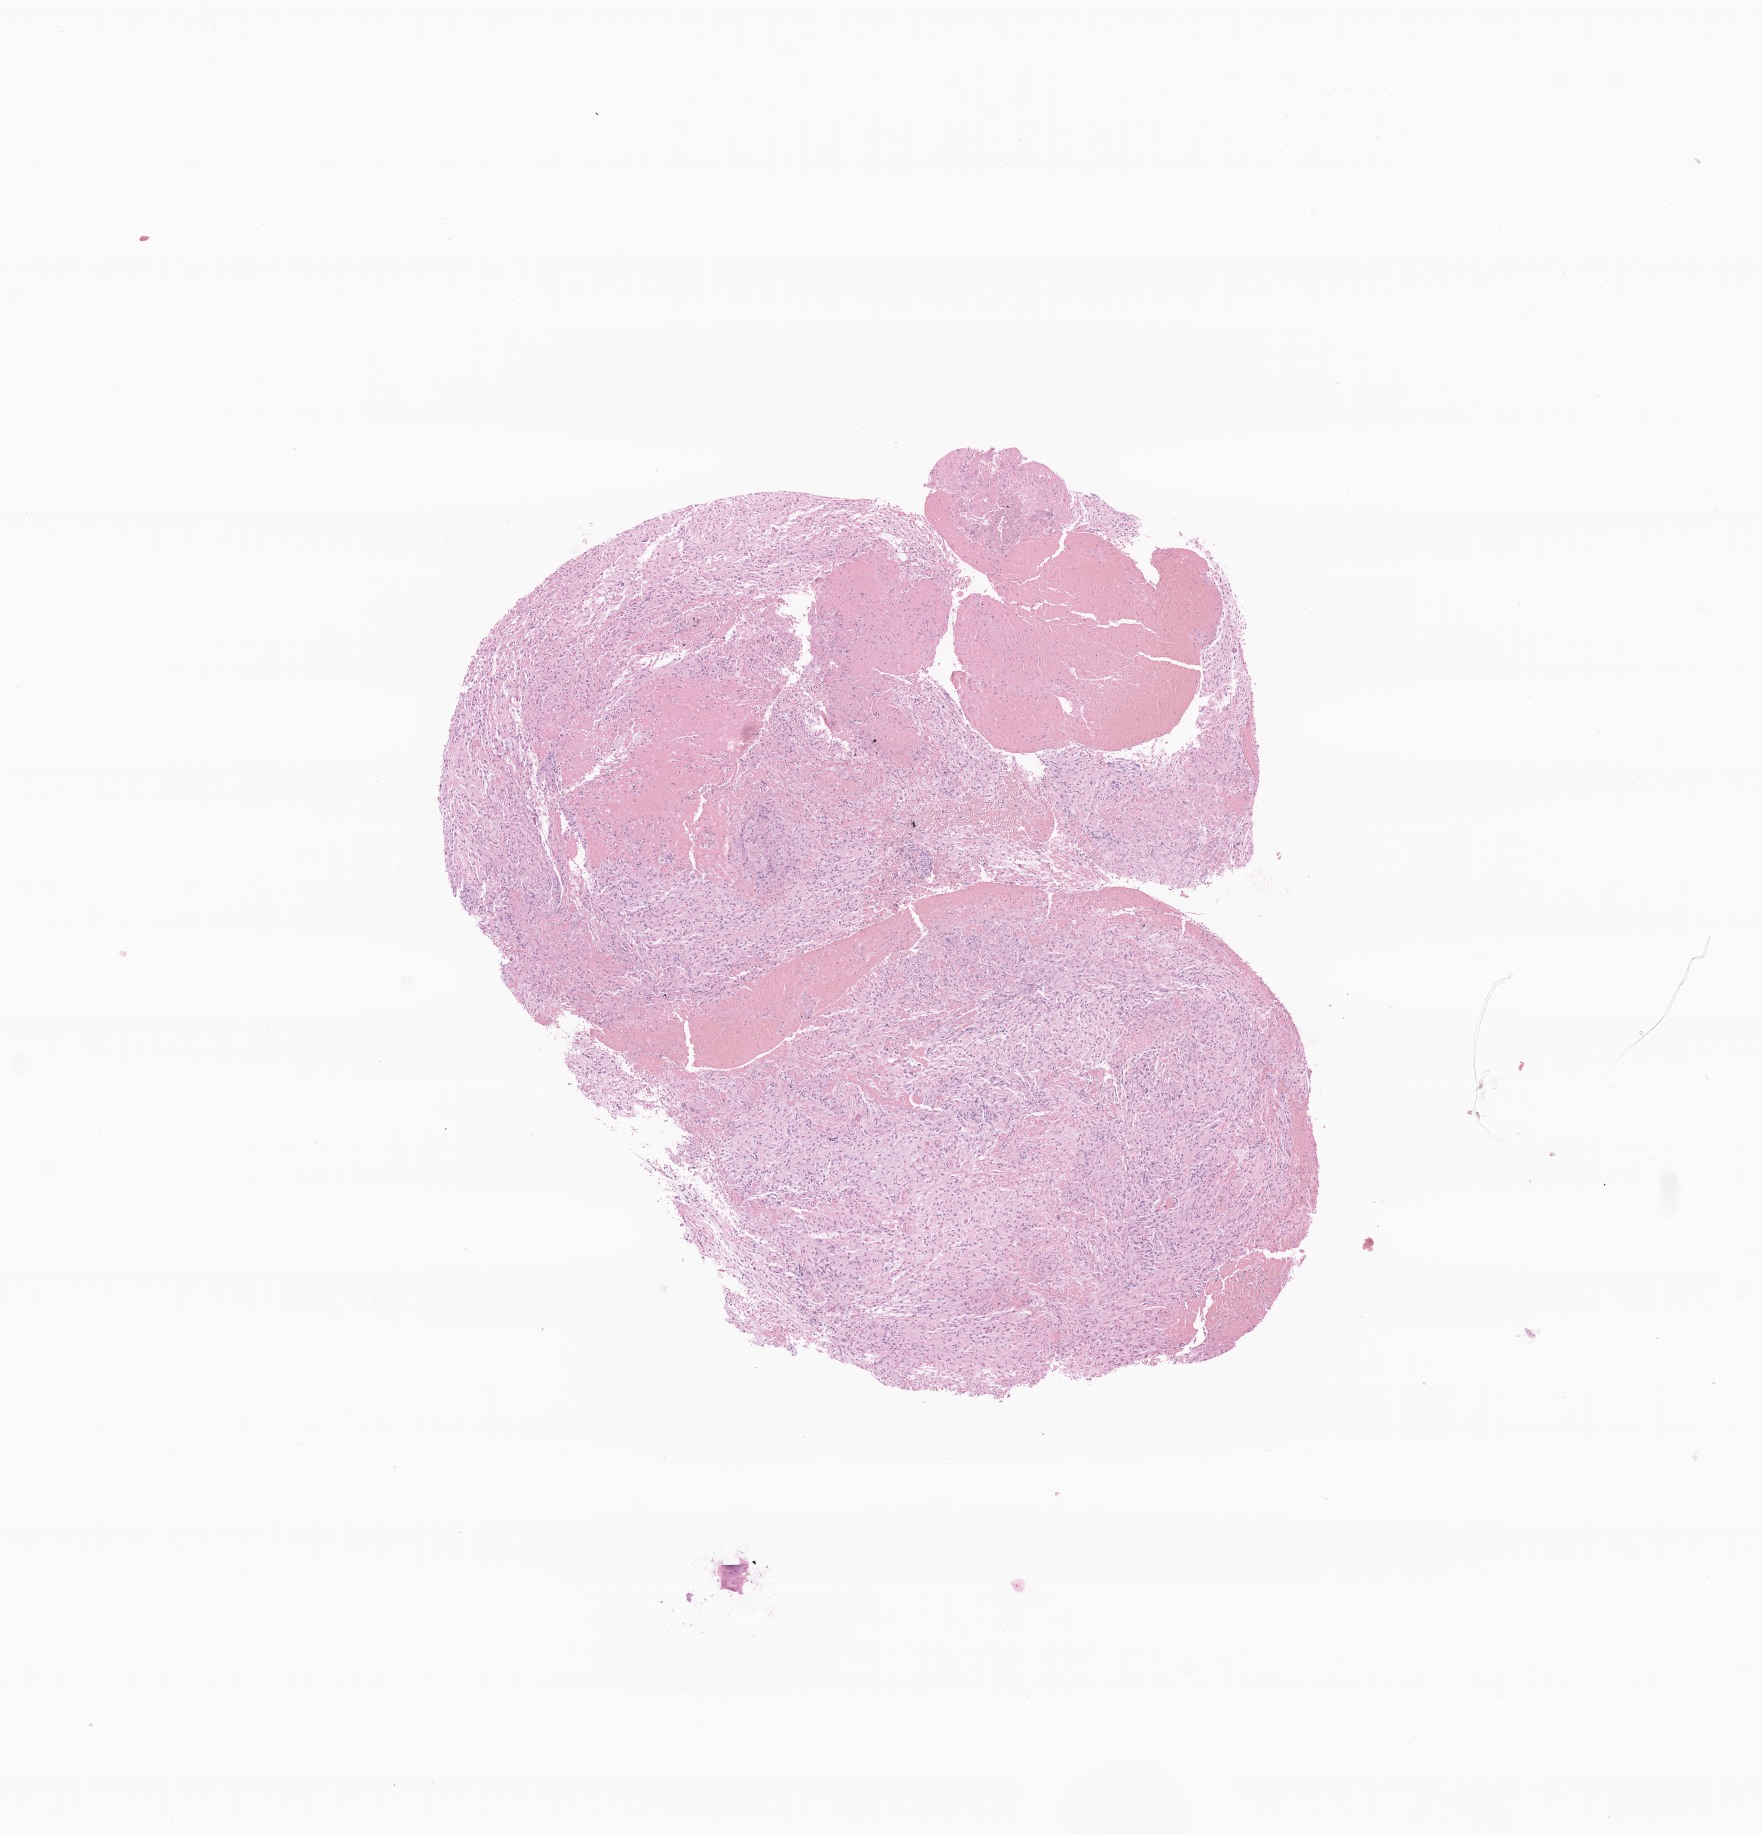
H&E whole-slide image of tumor tissue from the brain — whole scanned area (about 7.4 x 7.7 mm) shown as a low-resolution overview. Formalin-fixed, paraffin-embedded (FFPE) tissue. Patient: female, age 157 months (13 years 1 month).
Diagnosis: Pilocytic astrocytoma.